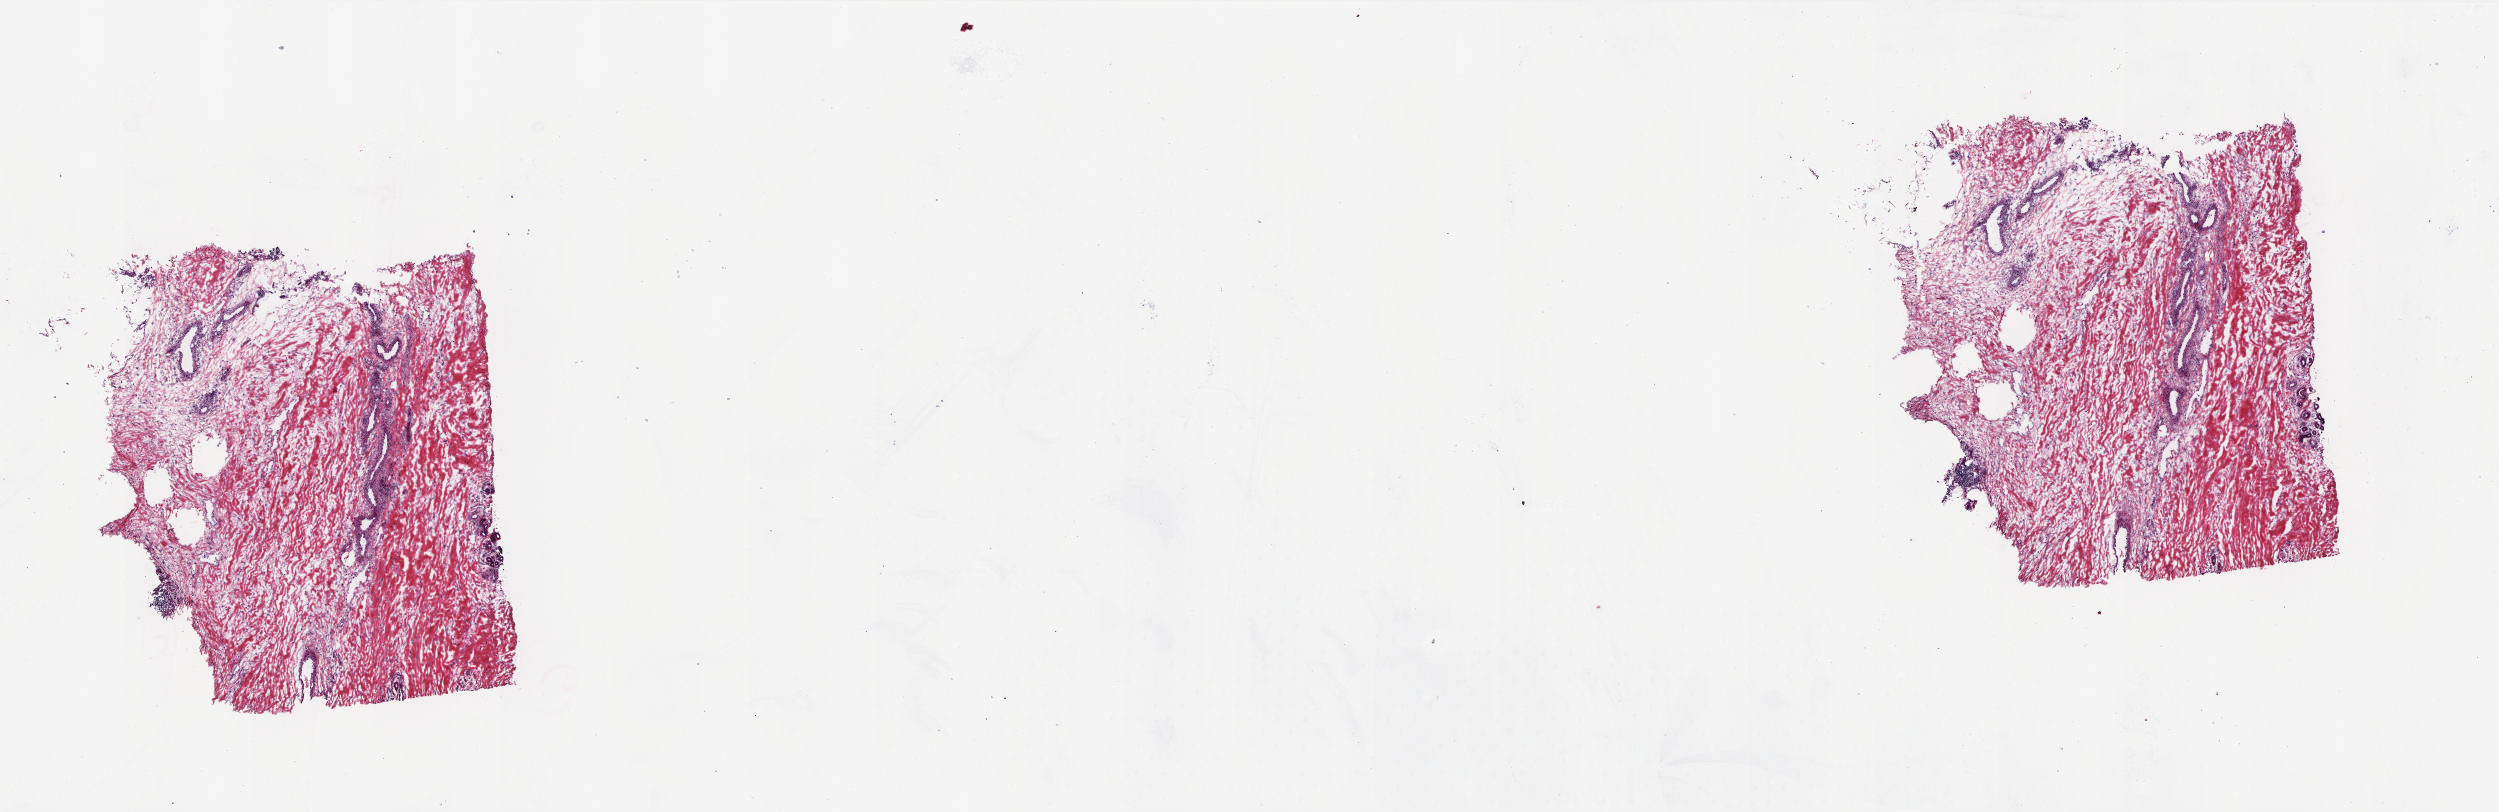
H&E-stained whole-slide image, shown as a low-resolution overview of the whole scanned area (about 20.0 x 6.5 mm, acquisition: 20x scan), frozen section from the top of the tissue portion, solid tissue normal (non-tumour tissue) sample from the bones, joints and articular cartilage of limbs. Patient: male, age at initial diagnosis 80 years.
This section: solid tissue normal (non-tumour) sample from the same patient. Patient diagnosis: Leiomyosarcoma, NOS (long bones of lower limb and associated joints).